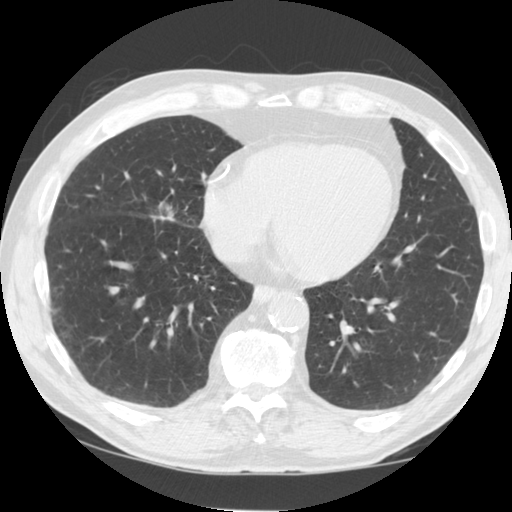
Low-dose screening chest CT, one axial slice. Position 38 of 125 along the scan axis. Lung window (W 1500 / L -600 HU). 2.5 mm slice thickness. 512 × 512 image matrix, field of view 350 × 350 mm.
Outlined on this slice (outlined manually by an expert reader):
- lesion 1 (tumor, middle lobe of right lung): bounding box [x1, y1, x2, y2] px = [157, 201, 174, 221]